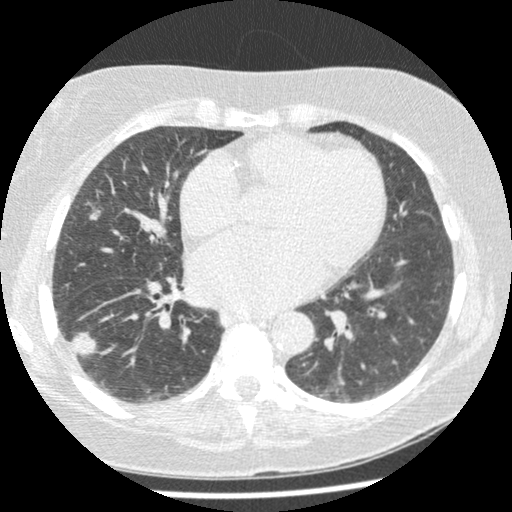
Low-dose screening chest CT, one axial slice; position 110 of 241 along the scan axis; reconstruction kernel STANDARD; 120 kVp; lung window (W 1500 / L -600 HU); 1.25 mm slice thickness; 512 × 512 image matrix, field of view 305 × 305 mm.
Outlined on this slice (manually delineated by an expert):
- lesion 1 (tumor, lower lobe of right lung): bounding box [x1, y1, x2, y2] px = [72, 331, 98, 356]